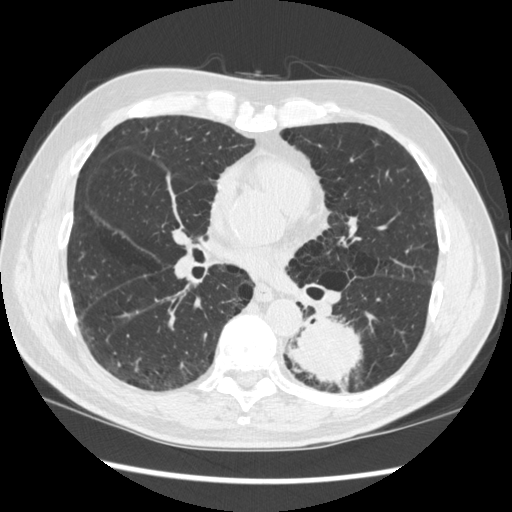
Chest CT (low-dose screening protocol), one axial image, first (baseline) screen, lung window (W 1500 / L -600 HU), 512 × 512 image matrix. Male, age 72 years at enrolment. Current smoker at enrolment.
- Expert-annotated lung lesion, box from (x=266, y=305) to (x=370, y=397) px.
- The screening reader recorded 2 non-calcified nodules or masses ≥4 mm on this exam; which of them this box marks is not recorded.